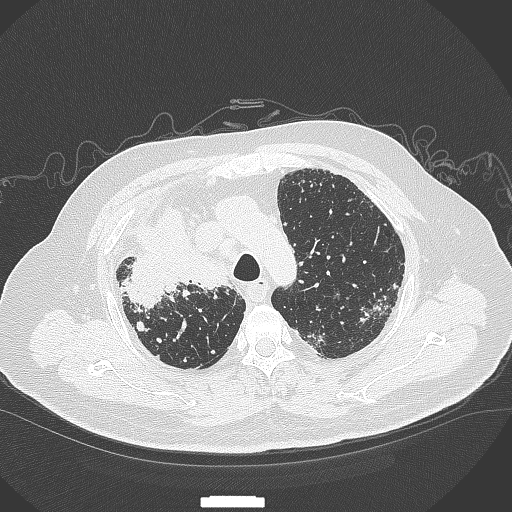
Chest CT, one axial slice. Slice 277 of 384 in the series (ordered by position). Reconstruction kernel B70f. Lung window (W 1500 / L -600 HU). 1 mm slice thickness. 512 × 512 image matrix, field of view 400 × 400 mm. Male patient, age 69 years. Case-level facts recorded for this patient, not image findings: clinical TNM (as recorded): T4 N3 M1.
Outlined on this slice (bounding box drawn by a radiologist):
- lung tumour (recorded histology: adenocarcinoma): bounding box (x1, y1, x2, y2) in pixels: (123, 206, 231, 311)